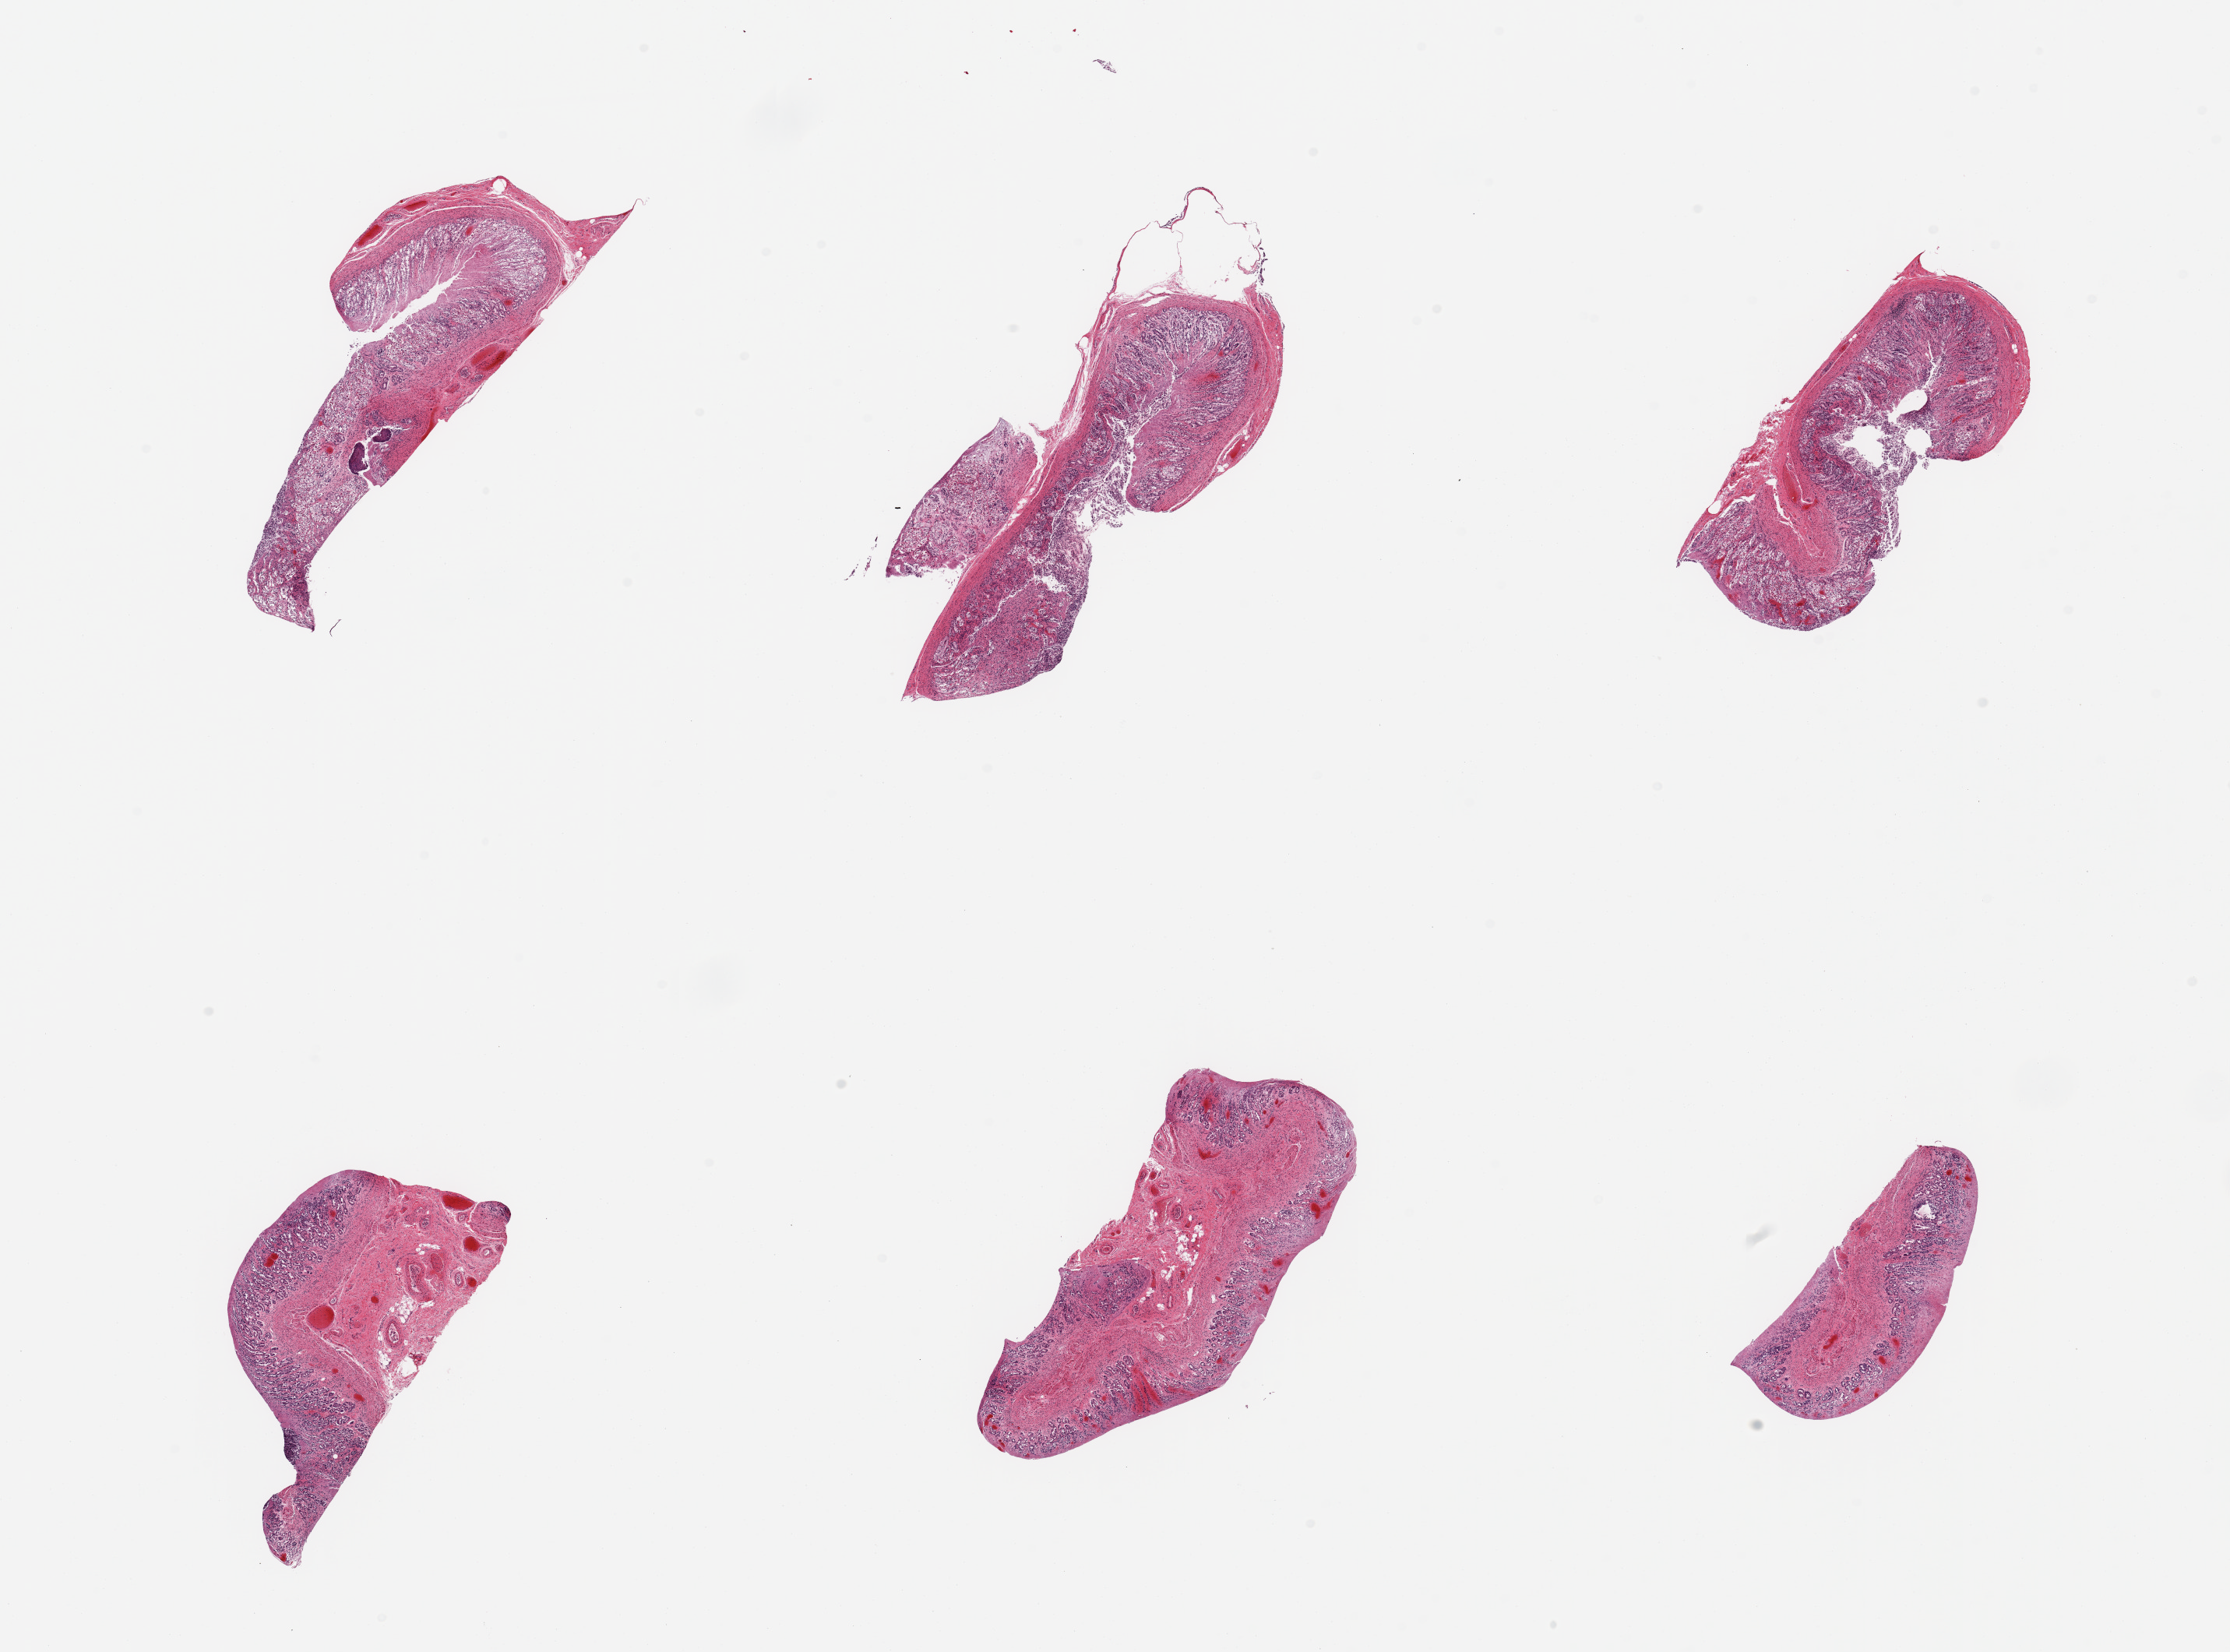
Digitized haematoxylin and eosin-stained section, brightfield — shown as a low-resolution overview of the whole scanned area (about 22.6 x 16.8 mm, acquisition: 20x scan). PAXgene-fixed paraffin-embedded (PFPE) section. Sampled site (target tissue): stomach. Donor tissue sample. Female donor.
Review note (as recorded): 6 pieces; moderate to severe mucosal autolysis.